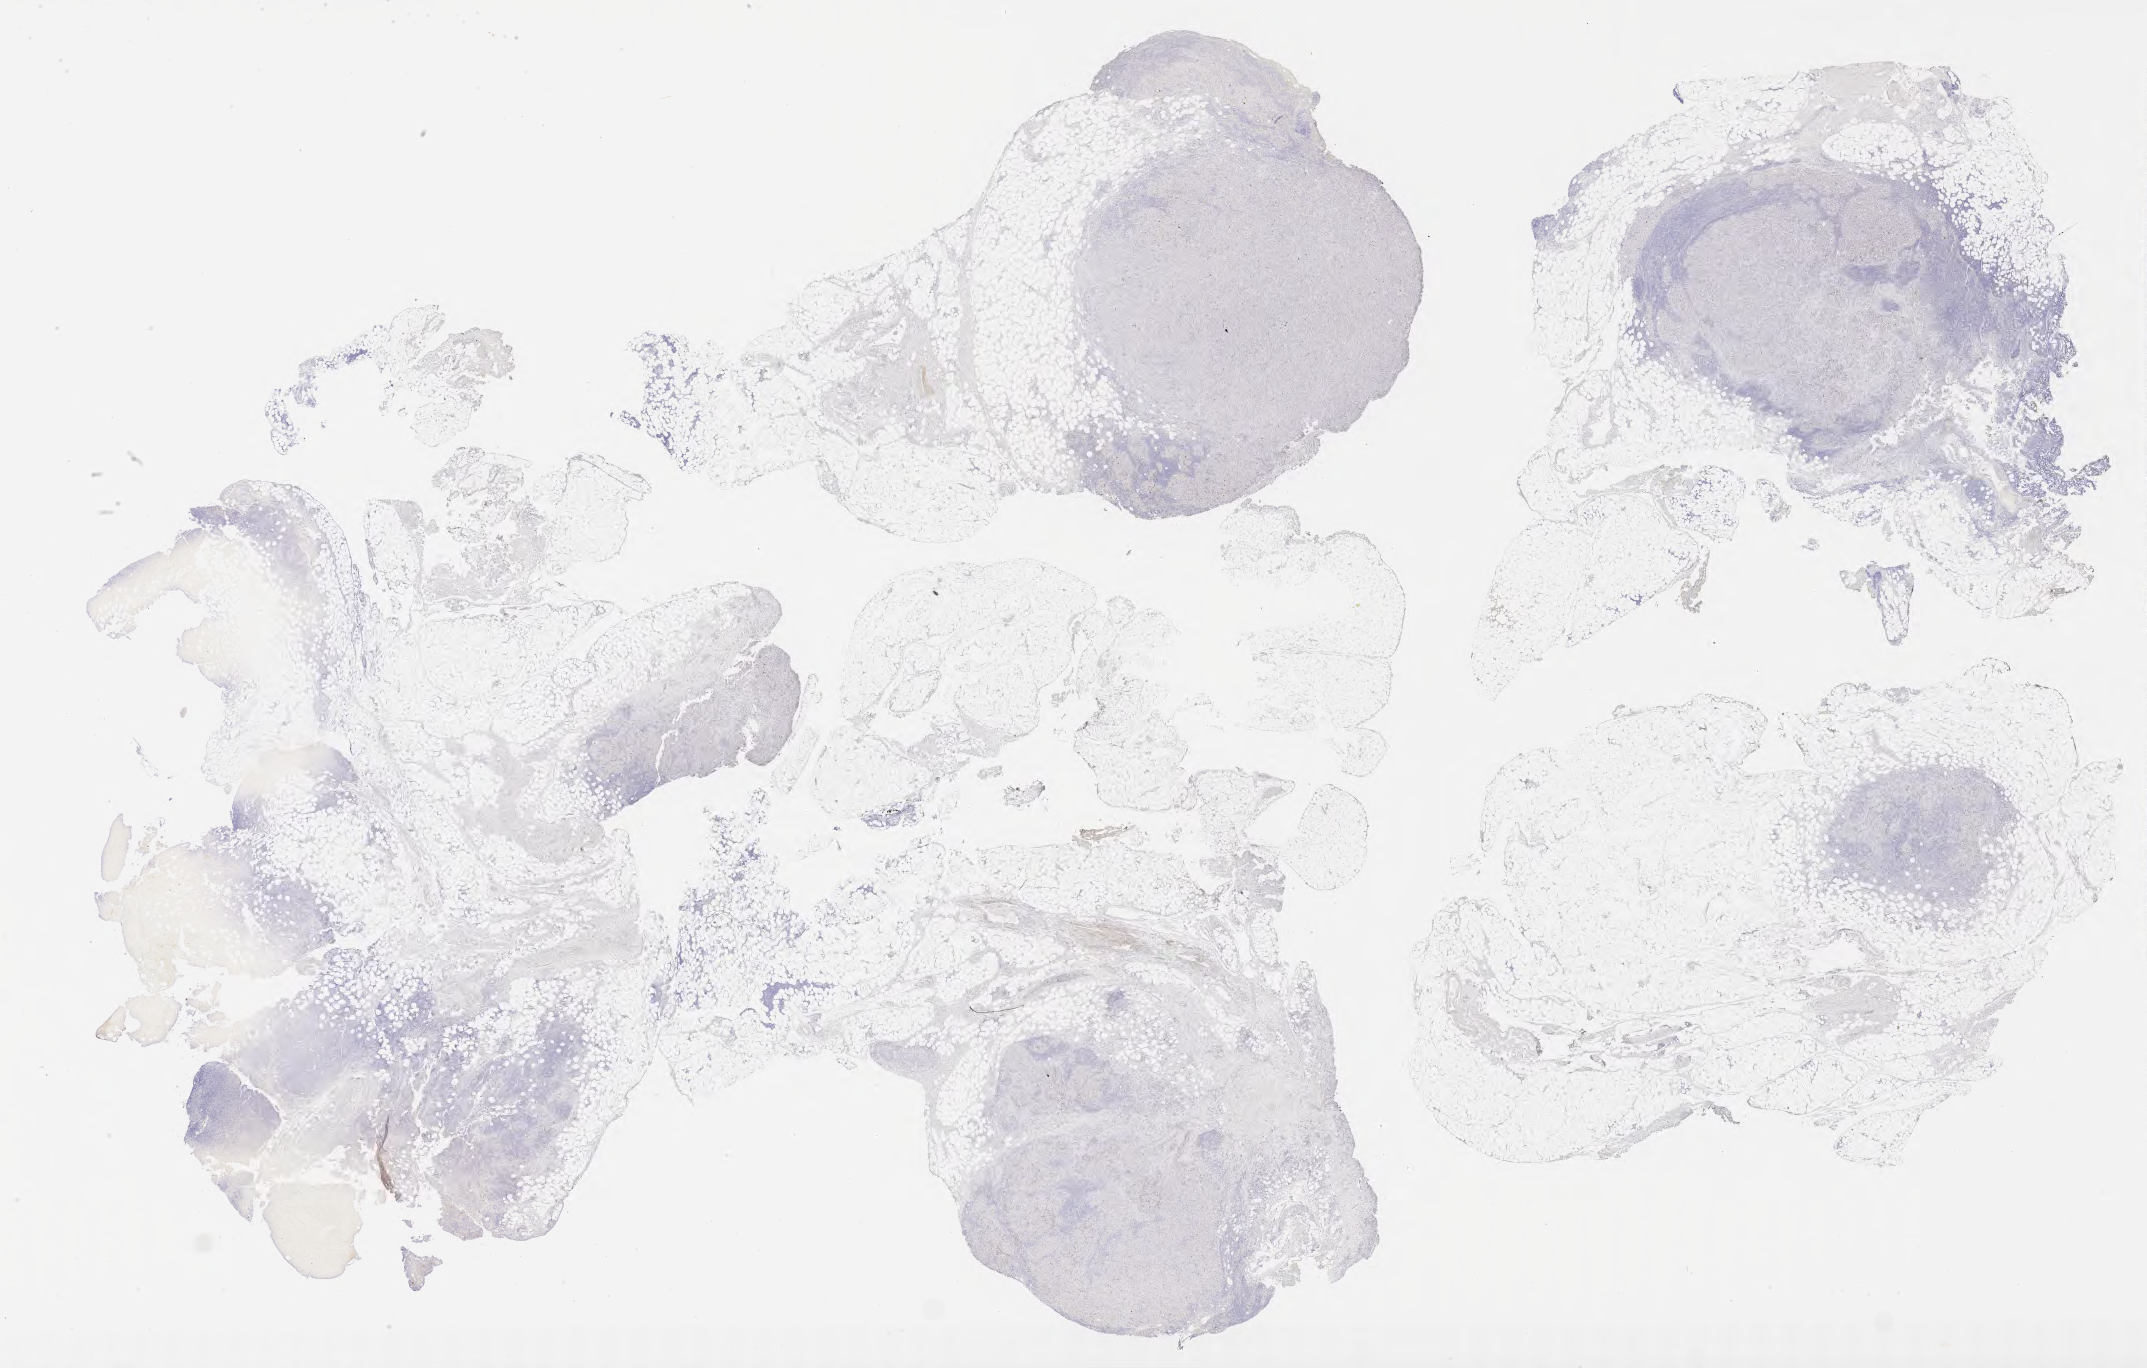
IHC for p40, whole-slide image, low-resolution overview of the scanned area, about 34.7 x 22.1 mm; specimen: tumor tissue; anatomic site: lung. Patient: male, aged 58.
Diagnosis: Adenocarcinoma, NOS.